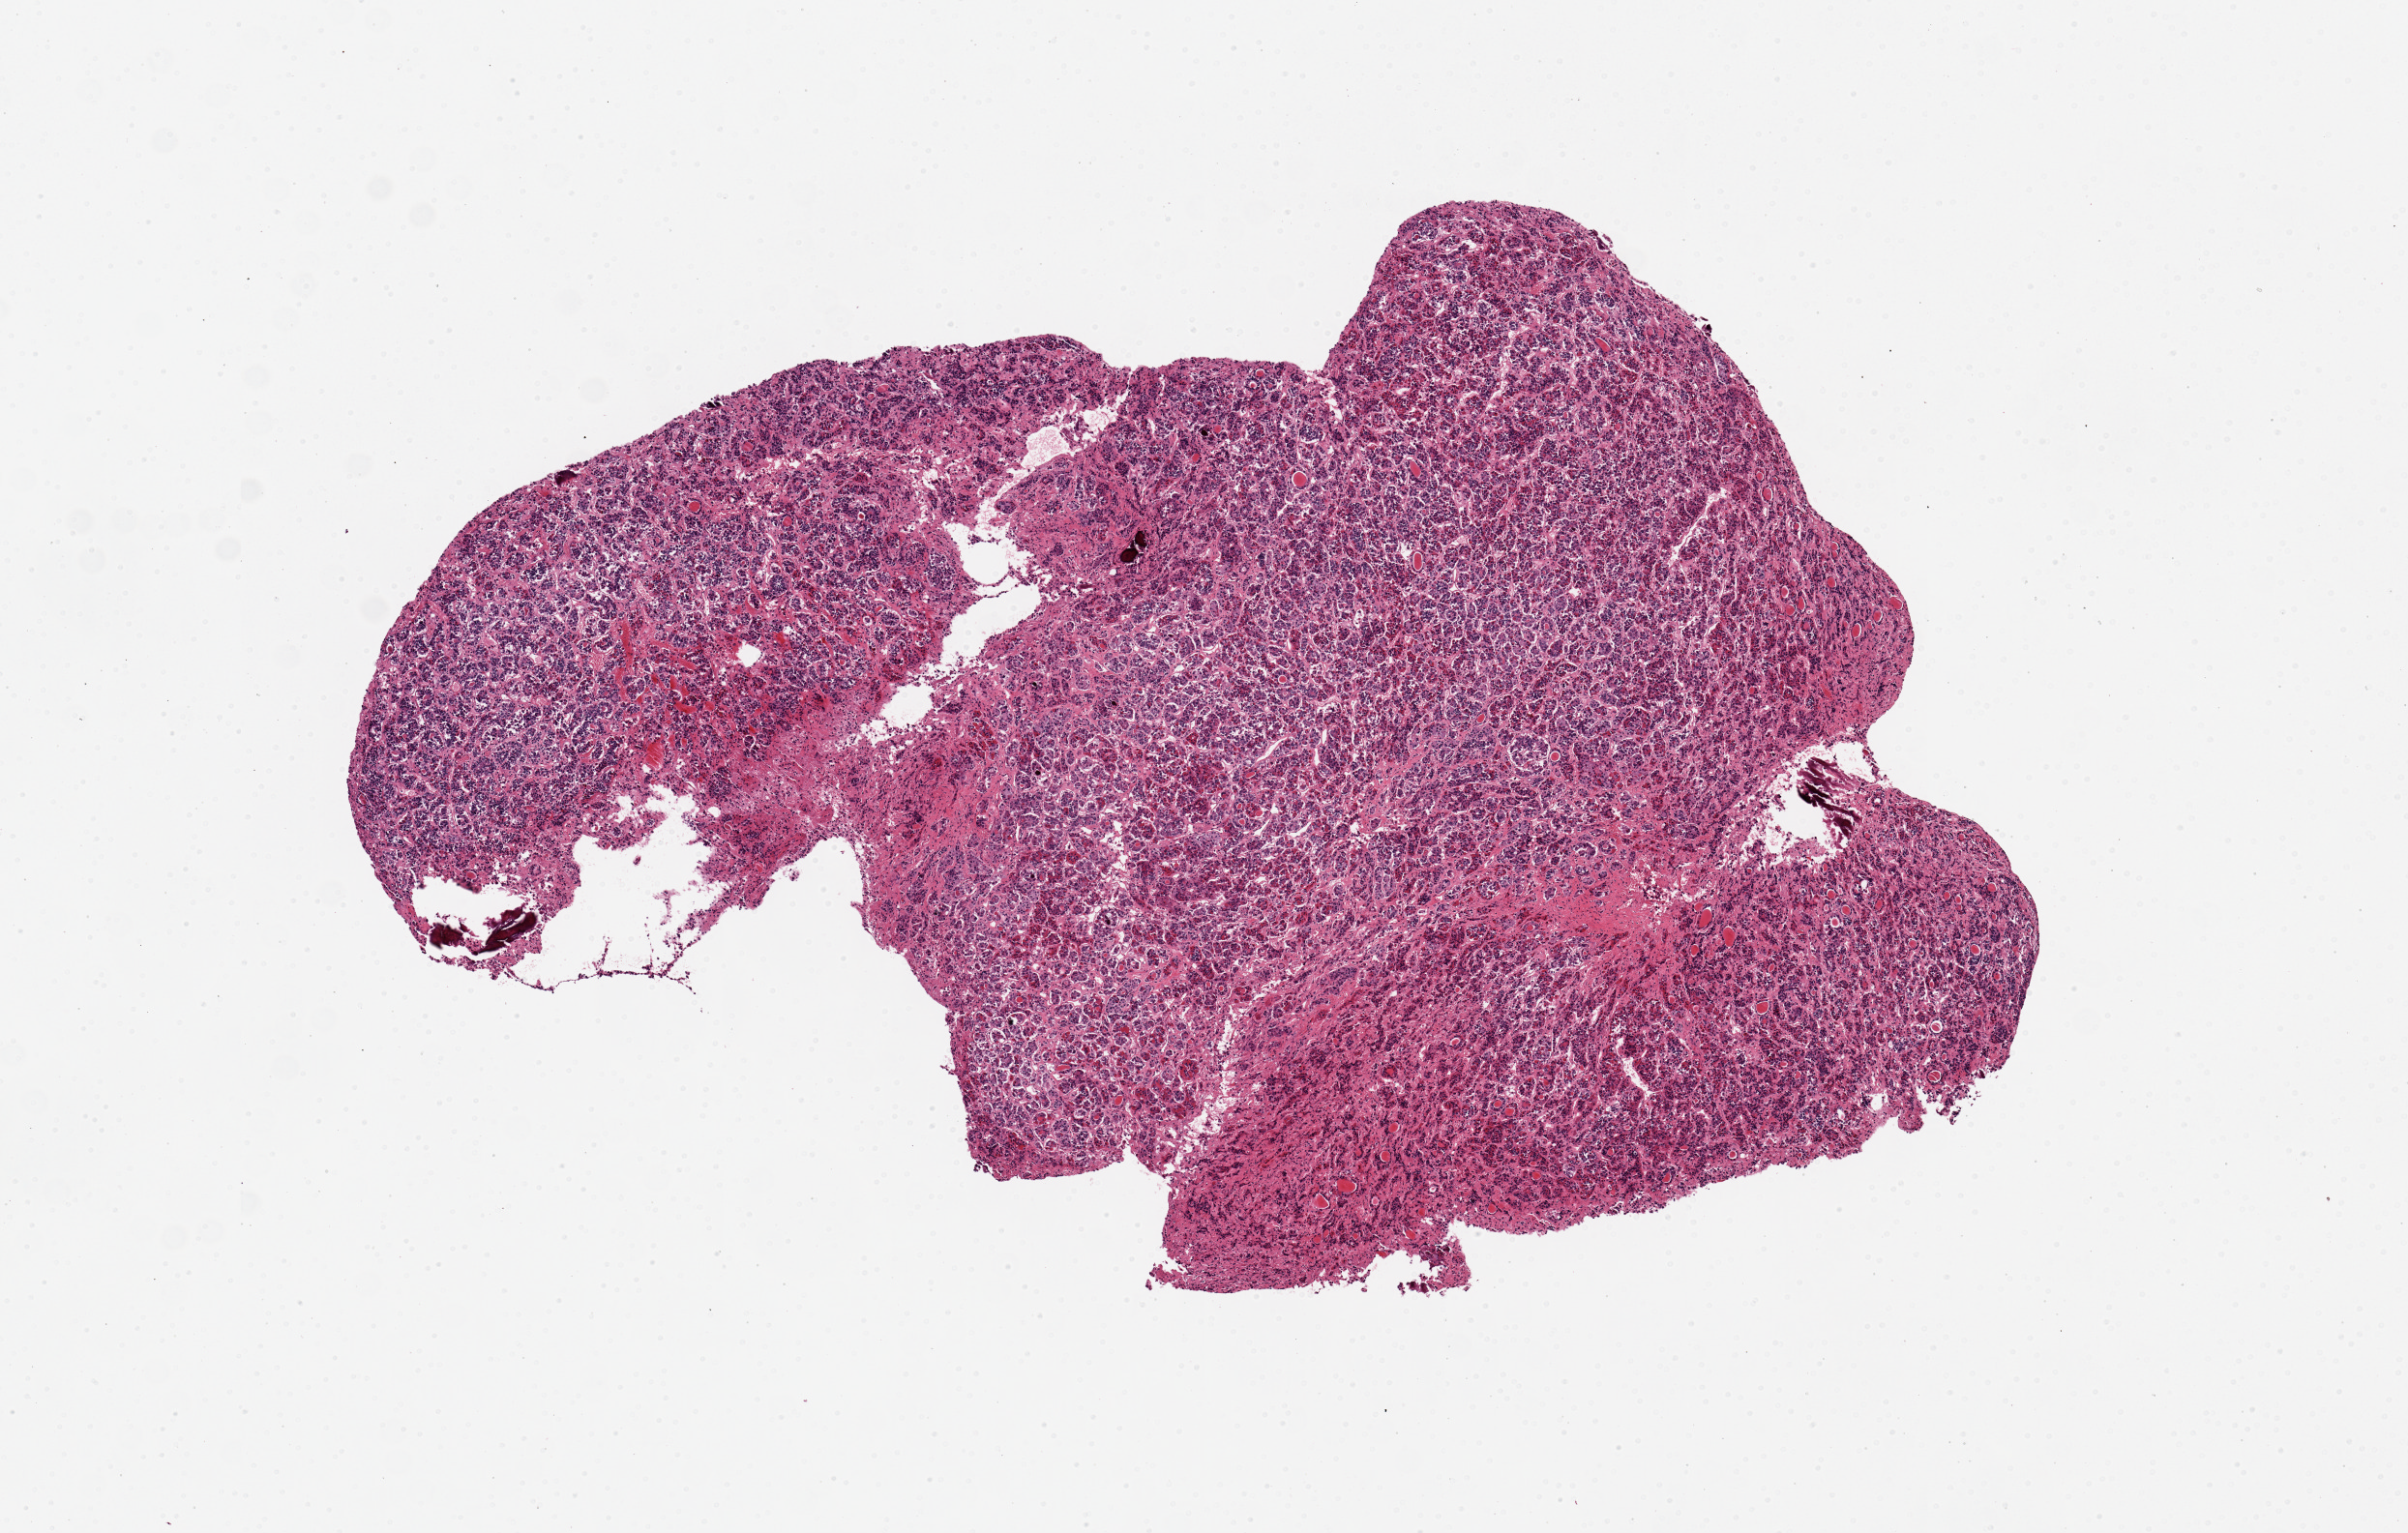
Digitized H&E-stained section, brightfield, shown as a low-resolution overview of the whole scanned area (about 9.8 x 6.3 mm, slide scanned at 20x); PAXgene-fixed, paraffin-embedded tissue; target tissue: pituitary; donor tissue sample. Donor: male.
Review note (as recorded): 1 piece.